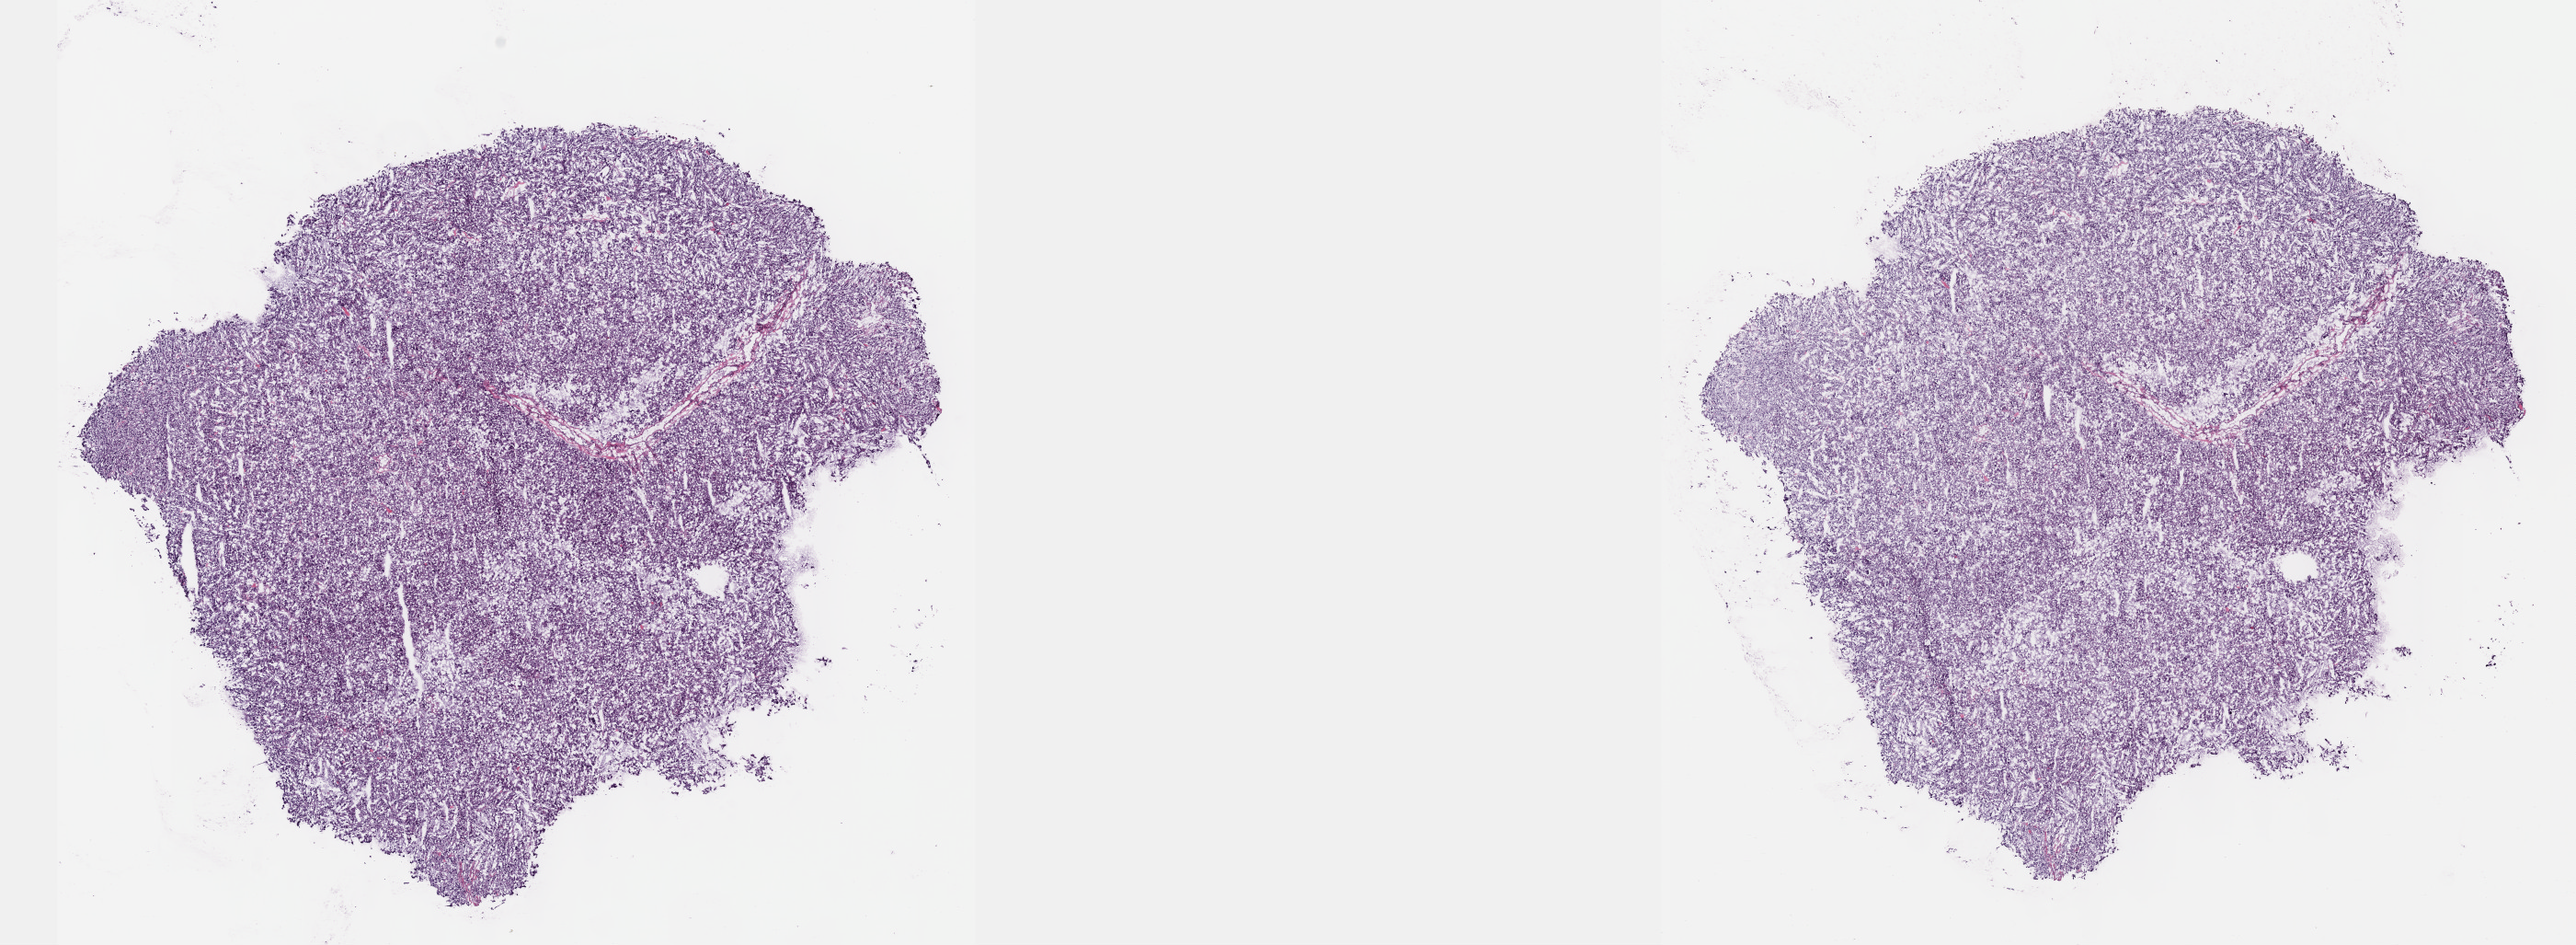
Whole-slide histology image, Hematoxylin and eosin (H&E) stained, shown as a low-resolution overview of the whole scanned area (about 22.6 x 8.3 mm). Frozen section. Adrenal gland, primary tumour sample. Female patient; age at initial diagnosis 63 years. Slide review estimates, as recorded: tumour cells 90%, tumour nuclei 95%, normal cells 0%, stromal cells 10%, necrosis 0%. Infiltration values recorded for this section: lymphocyte infiltration 0%, monocyte infiltration 0%, neutrophil infiltration 0%.
Laterality: left. Pathologic diagnosis: Pheochromocytoma, NOS.